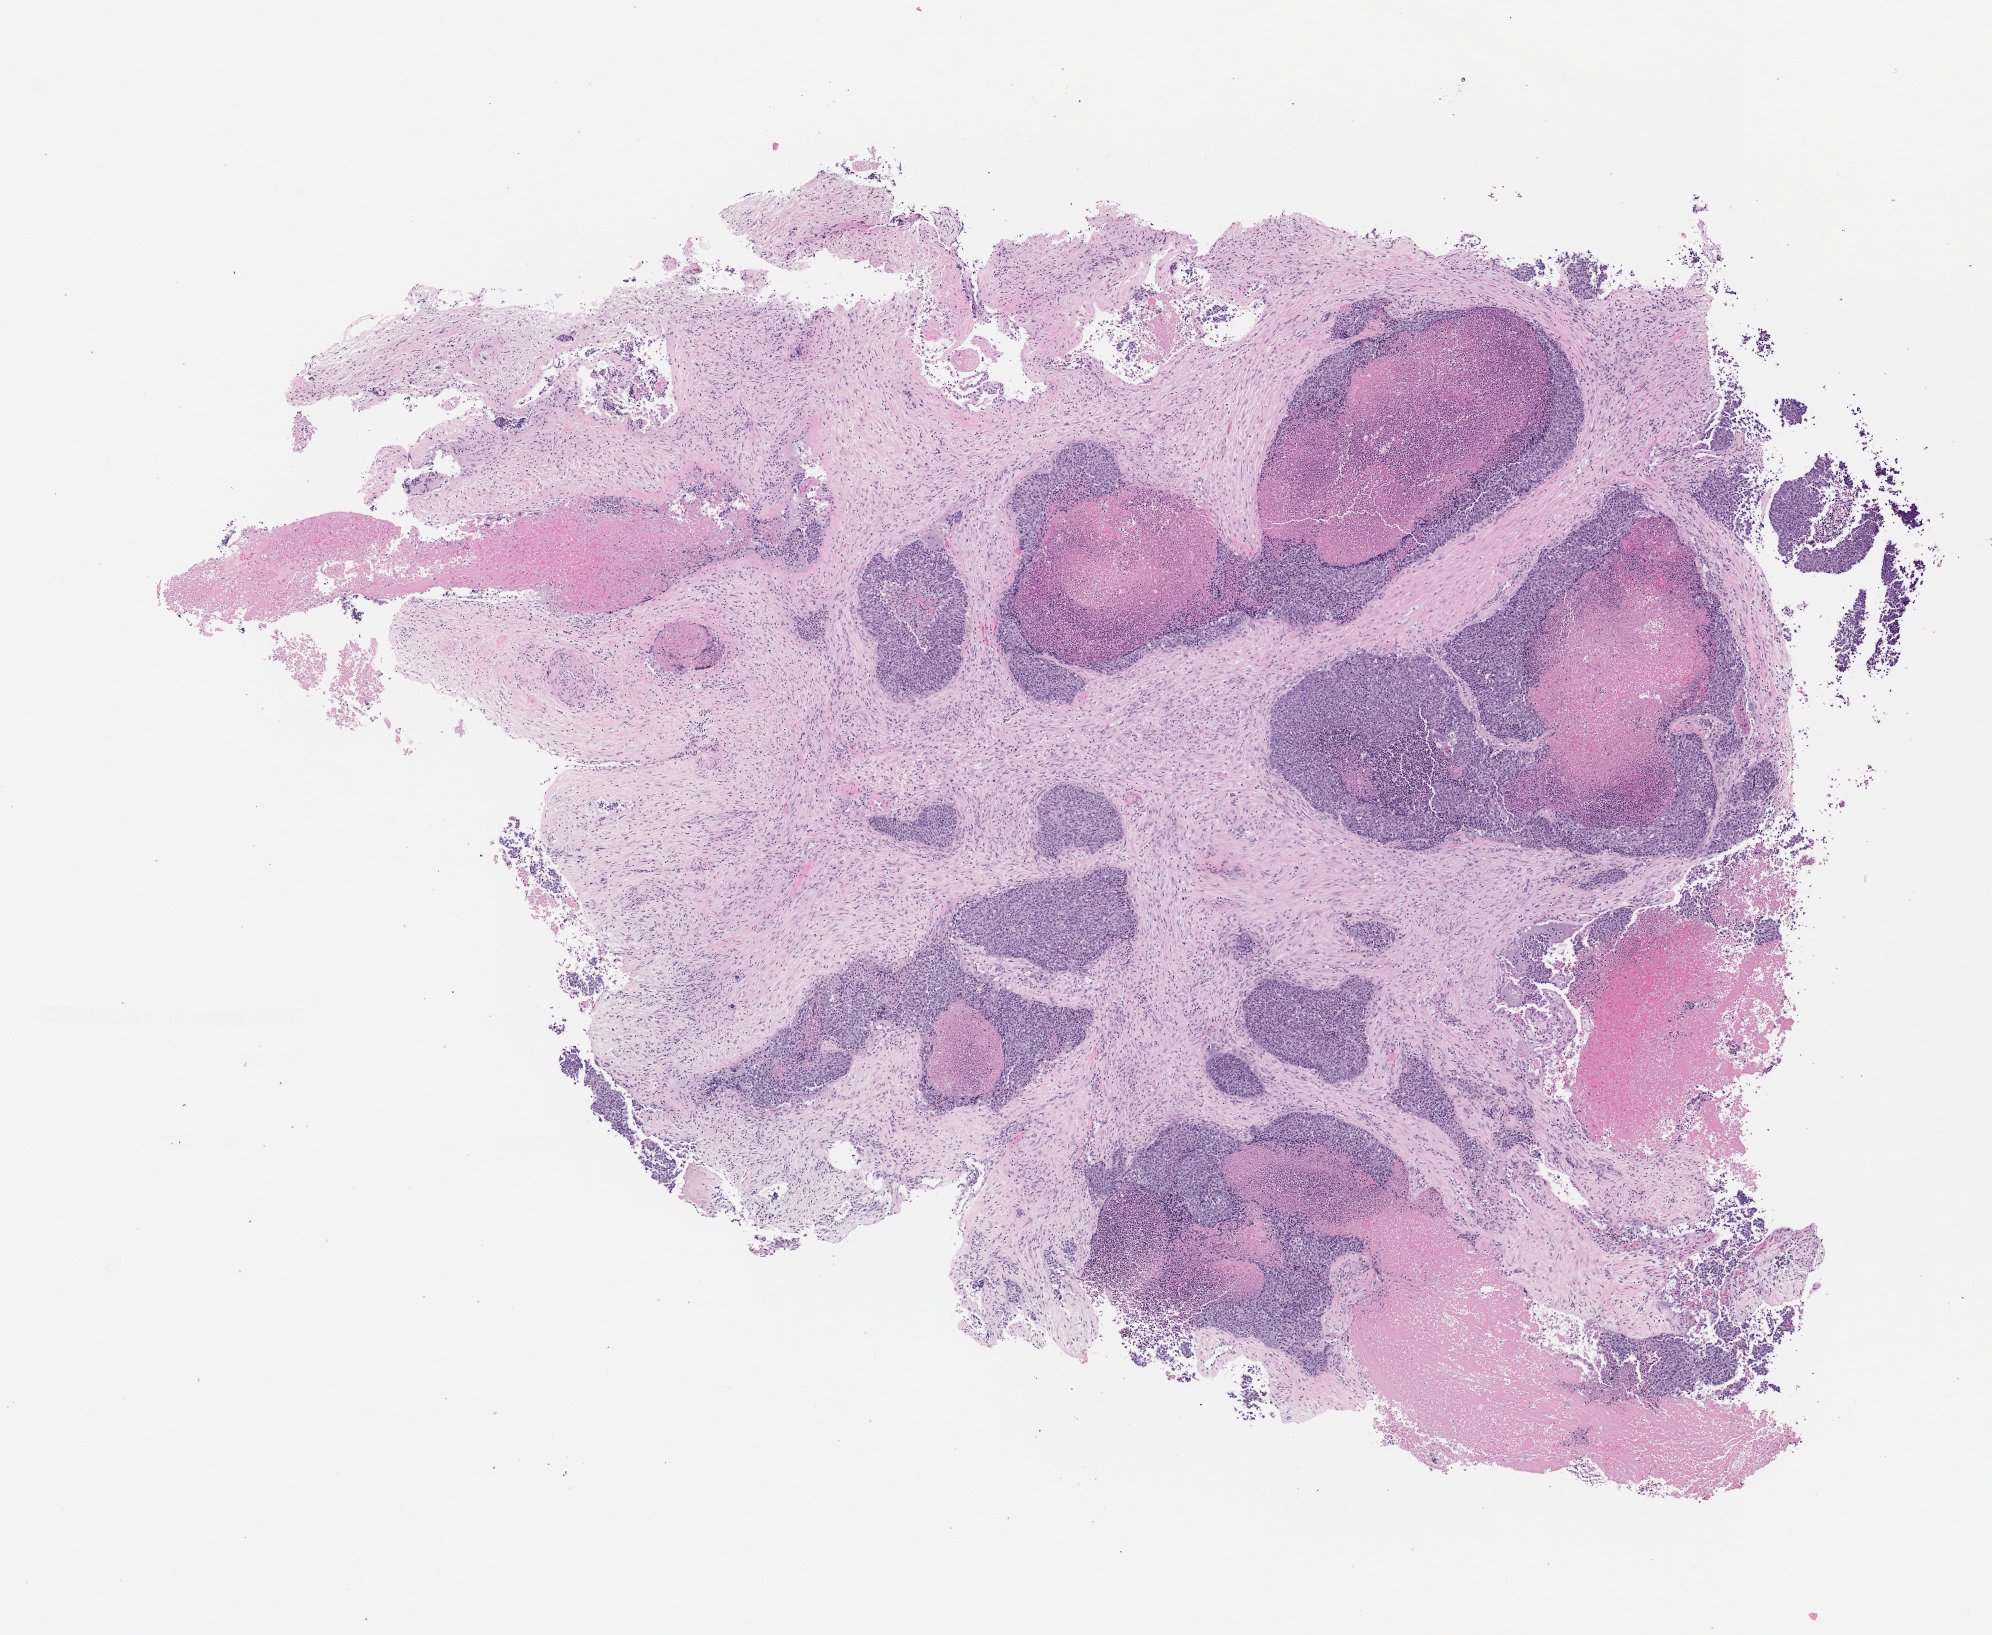
Digitized hematoxylin and eosin (H&E)-stained section of the patient's (originator) tumor tissue — shown as a low-resolution overview of the whole scanned area (about 8.0 x 6.6 mm); FFPE section; originating tumor site category: vagina. Female patient, 58 years old.
Diagnosis: Vaginal Carcinoma.